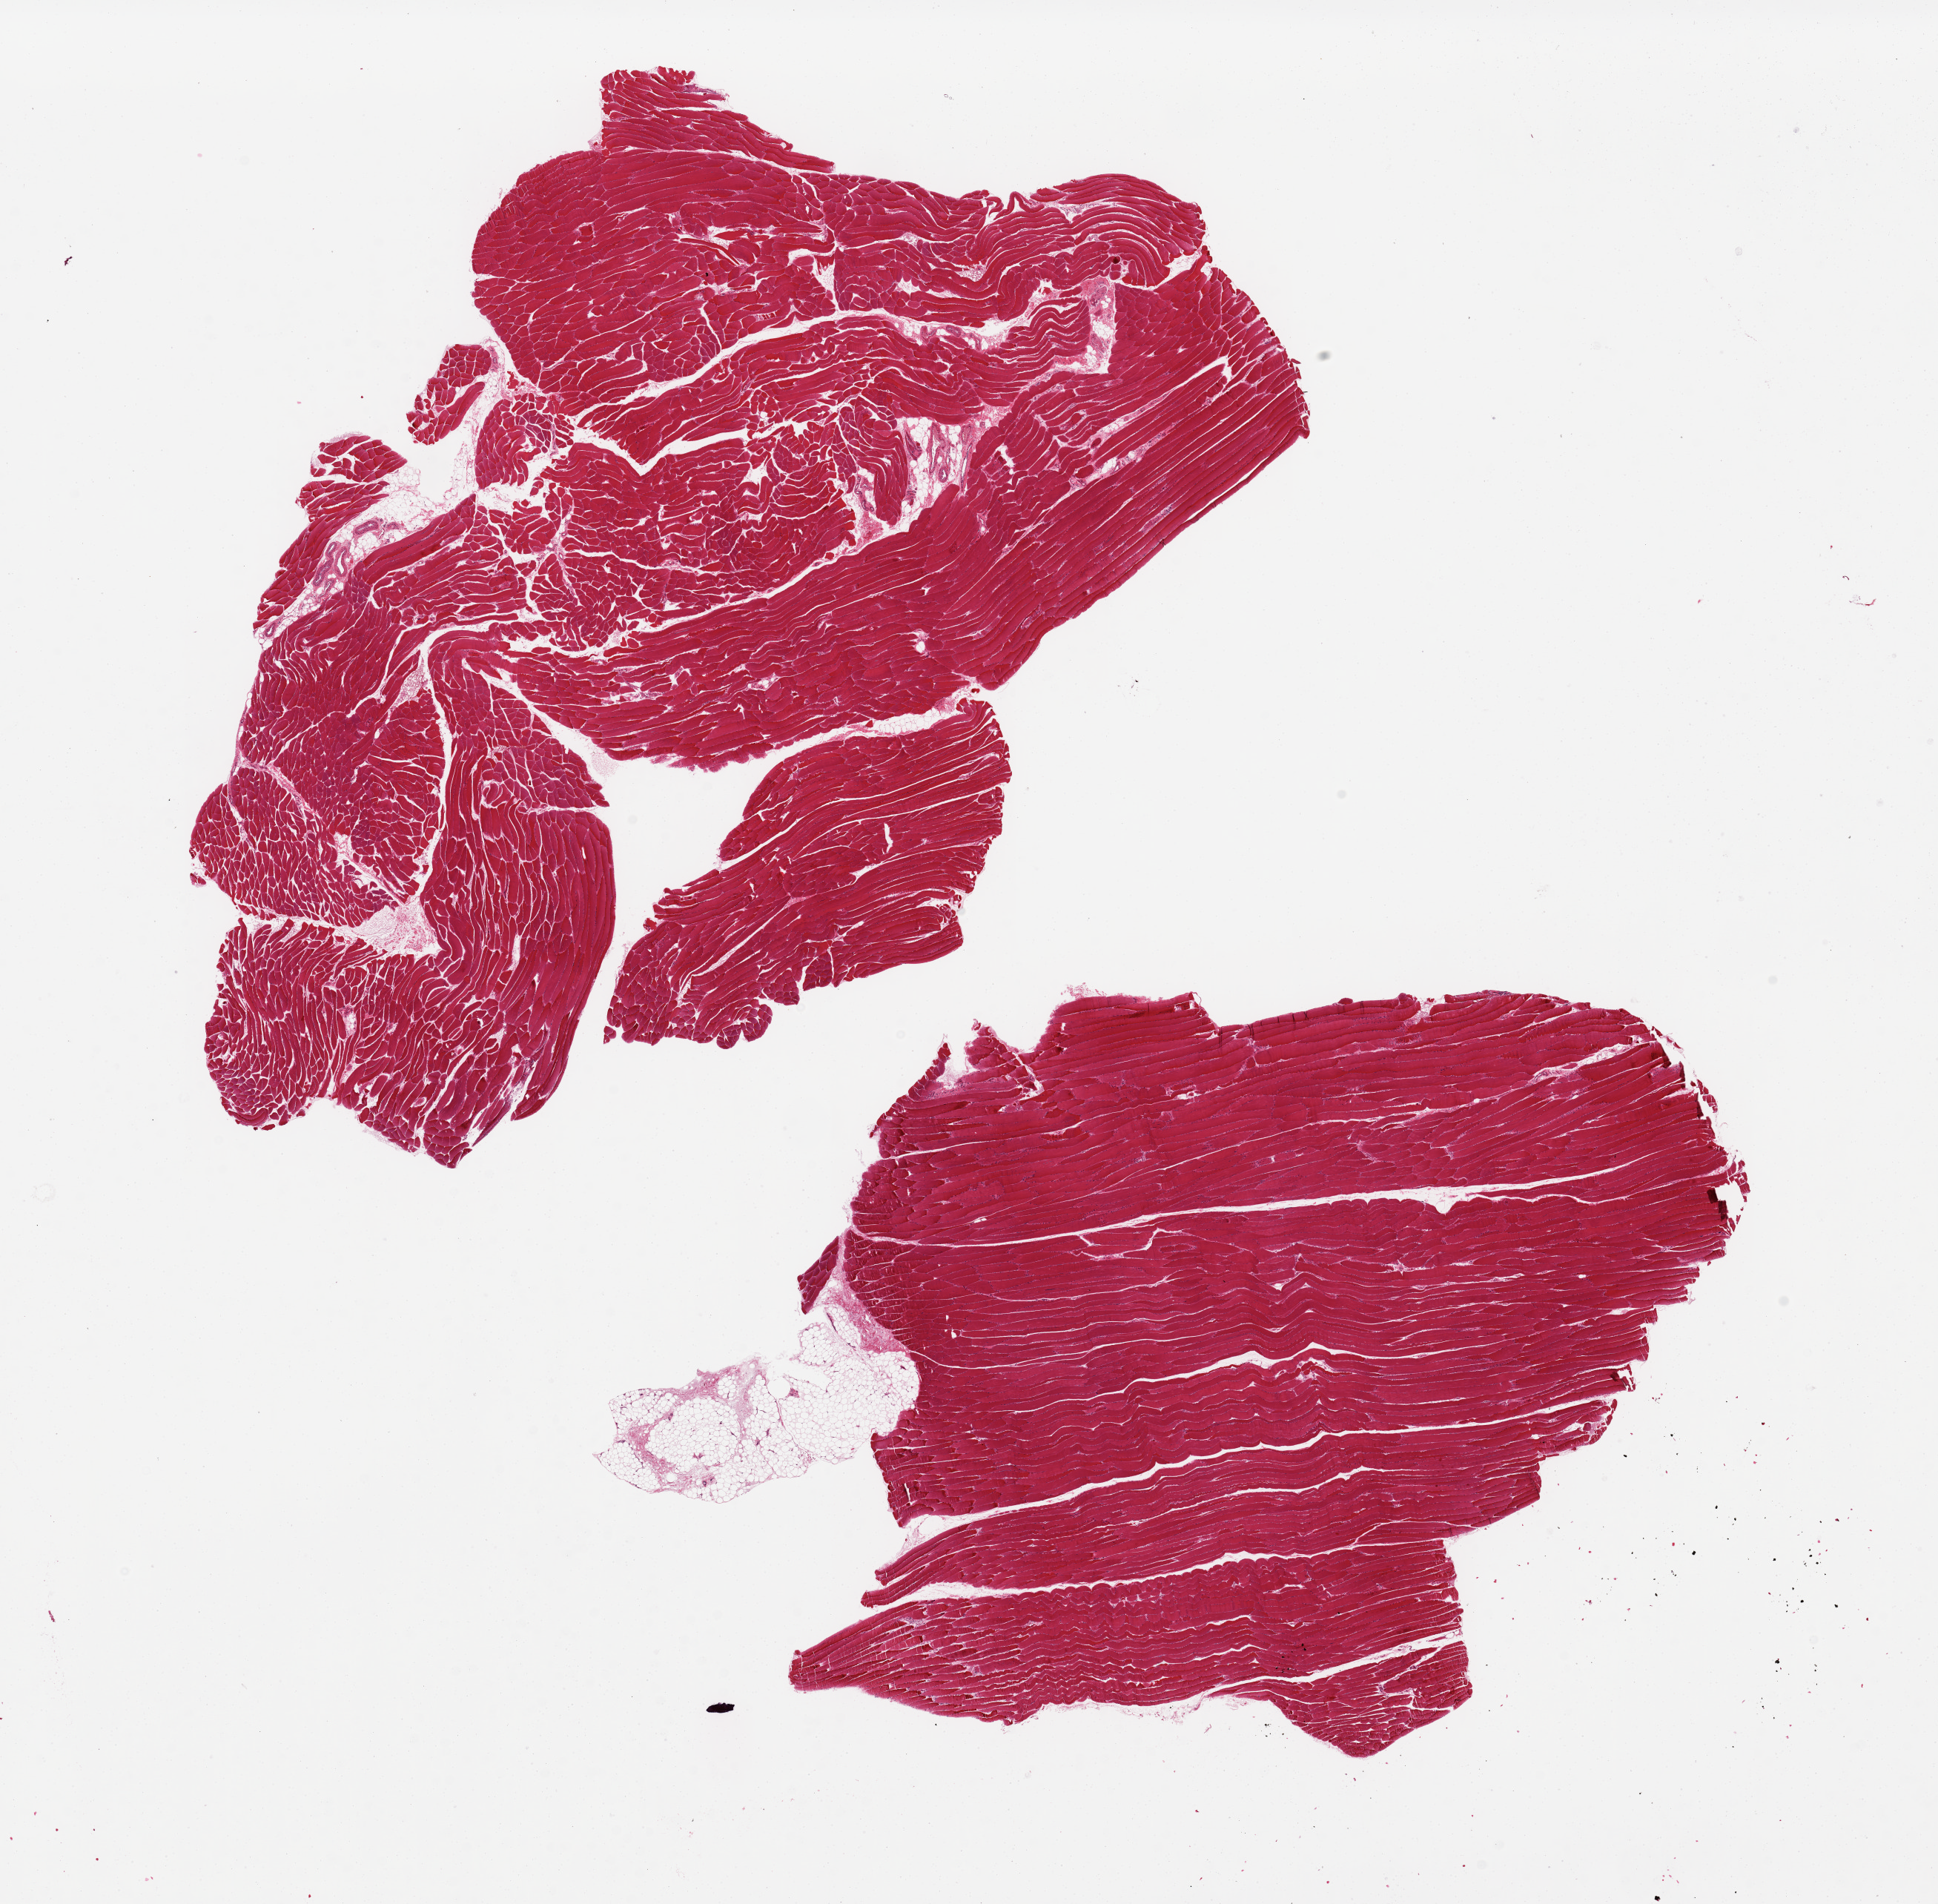
Whole-slide image, hematoxylin and eosin (H&E) stain — whole scanned area (about 20.7 x 20.3 mm, acquisition: 20x scan) shown as a low-resolution overview, PAXgene-fixed, paraffin-embedded tissue, sampled site (target tissue): skeletal muscle, tissue donor sample. Donor sex: male.
Pathologist's review note for this sample: 2 pieces. 14x9 & 12.5x9mm; Well trimmed, no adipose.